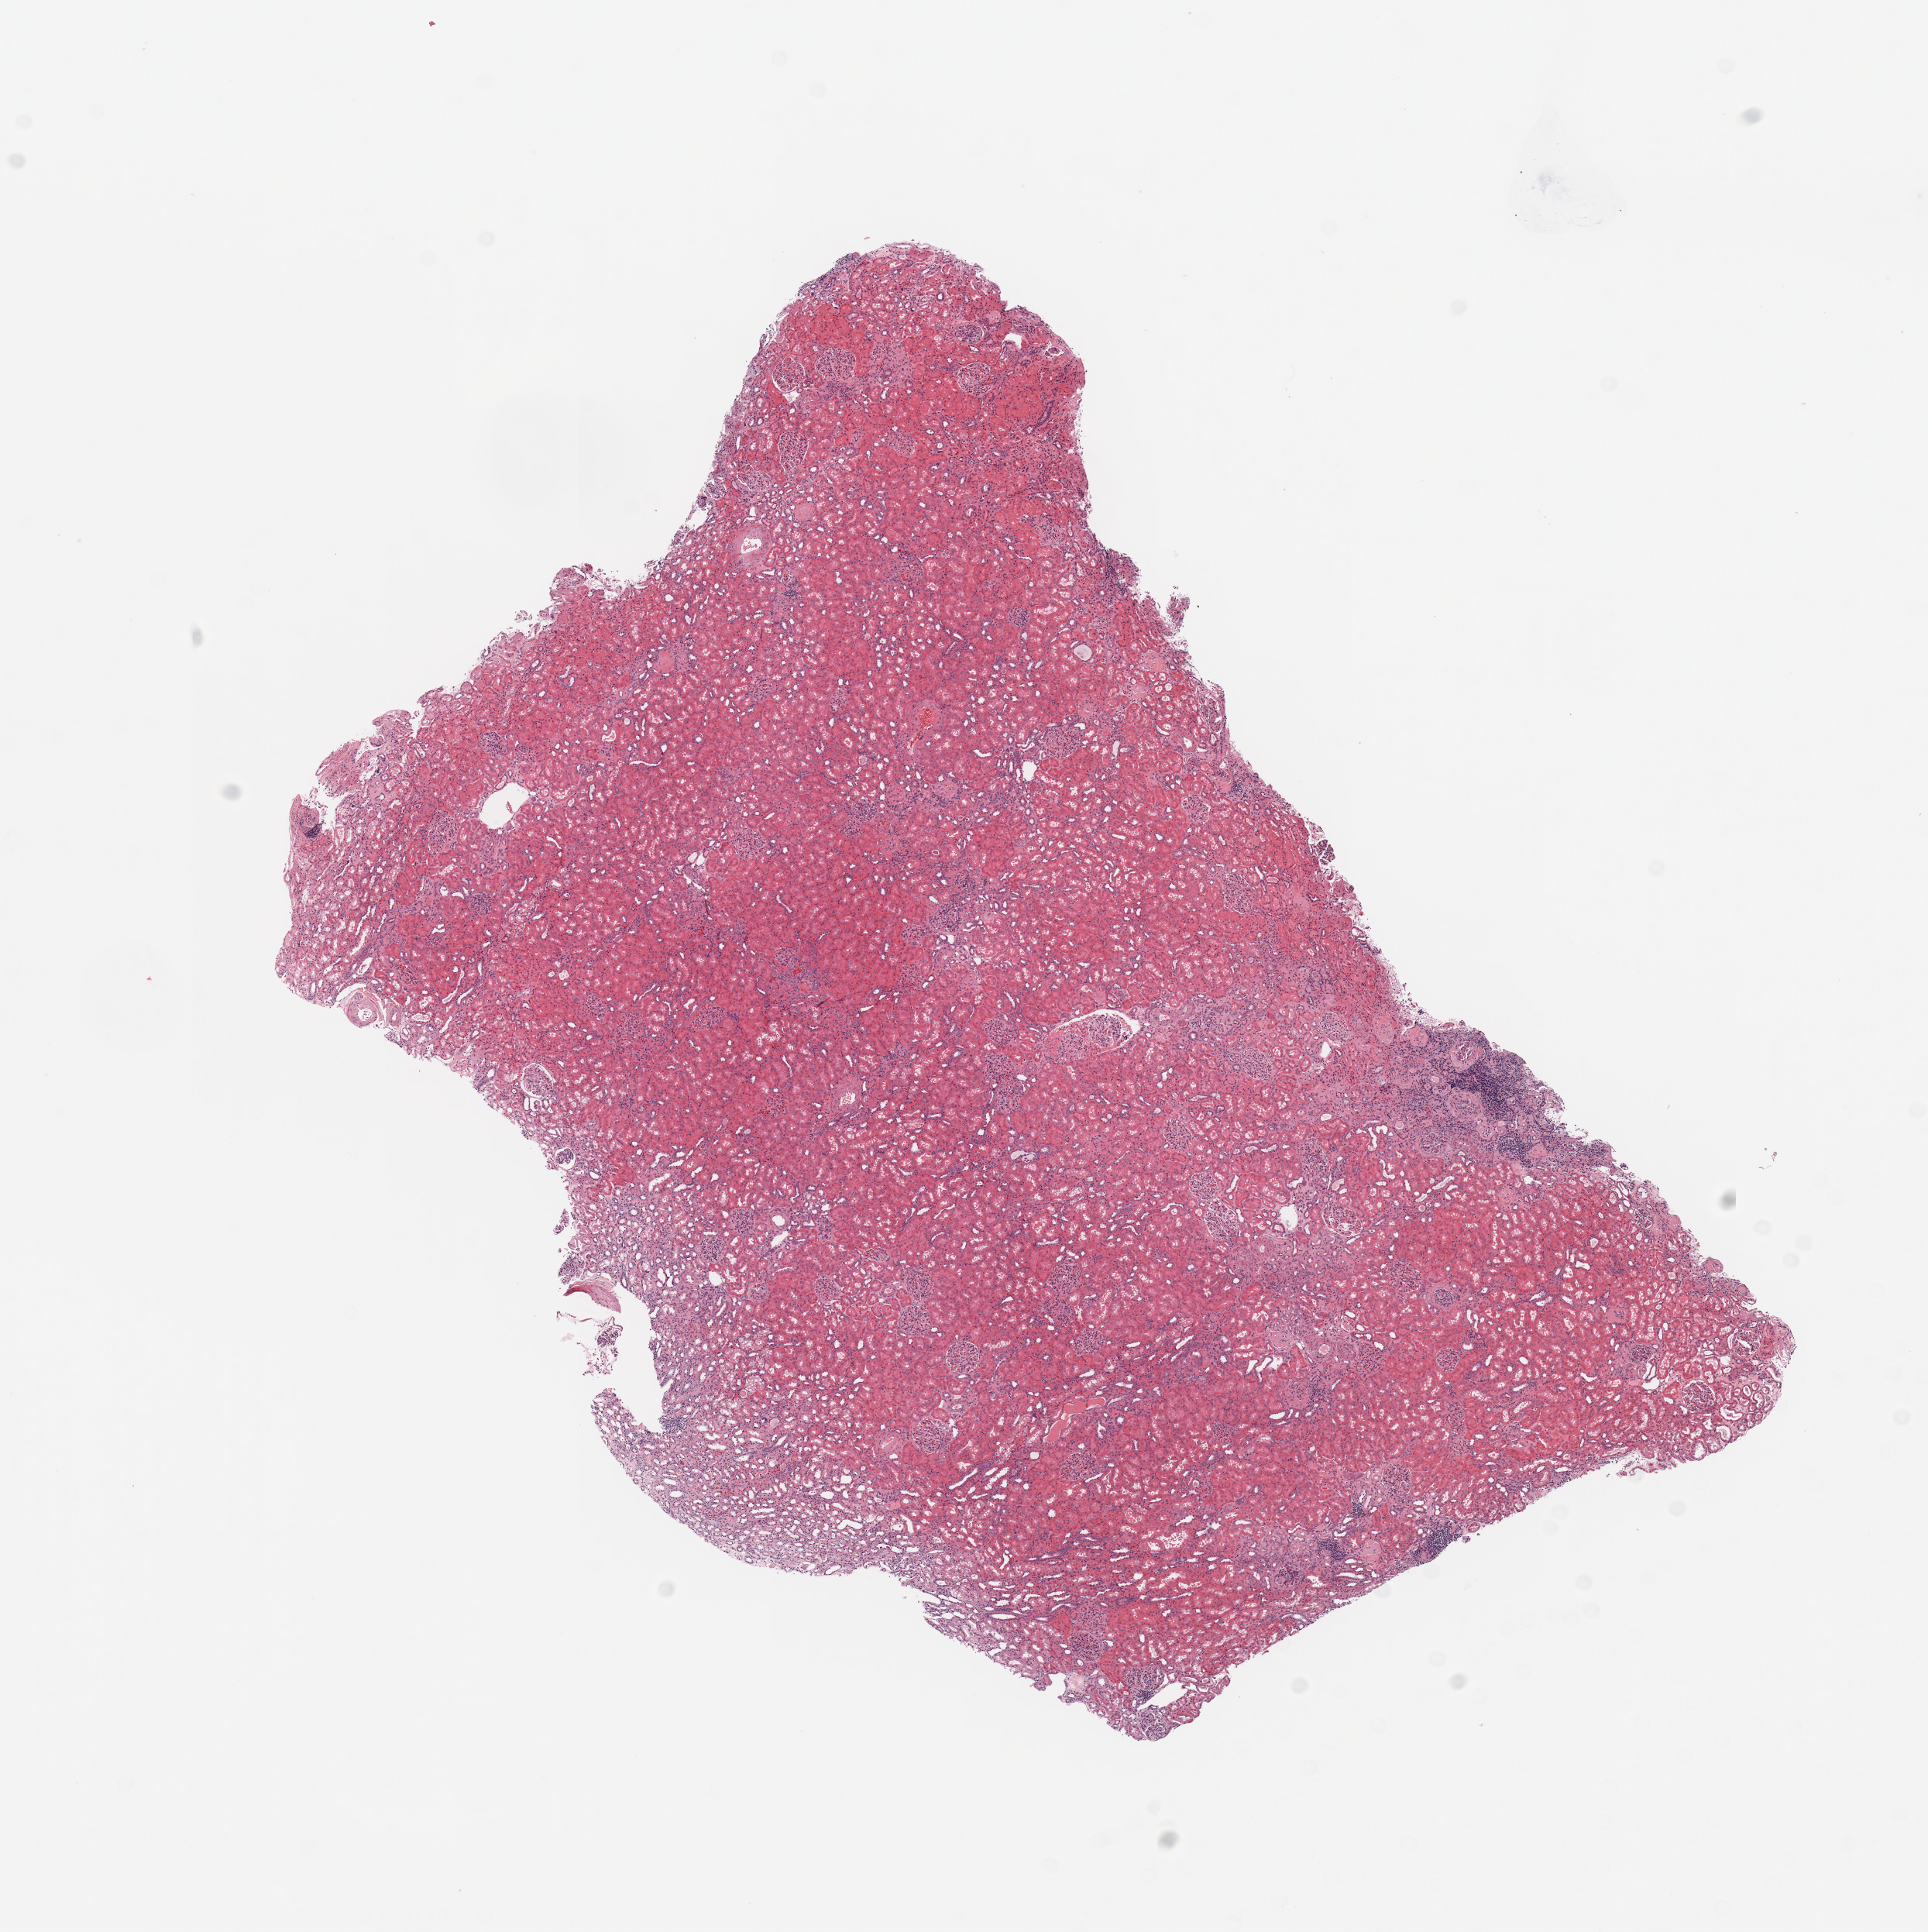
Whole-slide histology image, Hematoxylin and eosin (H&E) stained, a low-resolution overview of the entire scanned area, about 9.8 x 9.9 mm, normal (non-tumour) tissue sample, sampled site: kidney. 79-year-old female patient.
This section: normal (non-tumour) tissue from the same patient. Patient diagnosis: Renal cell carcinoma, NOS.